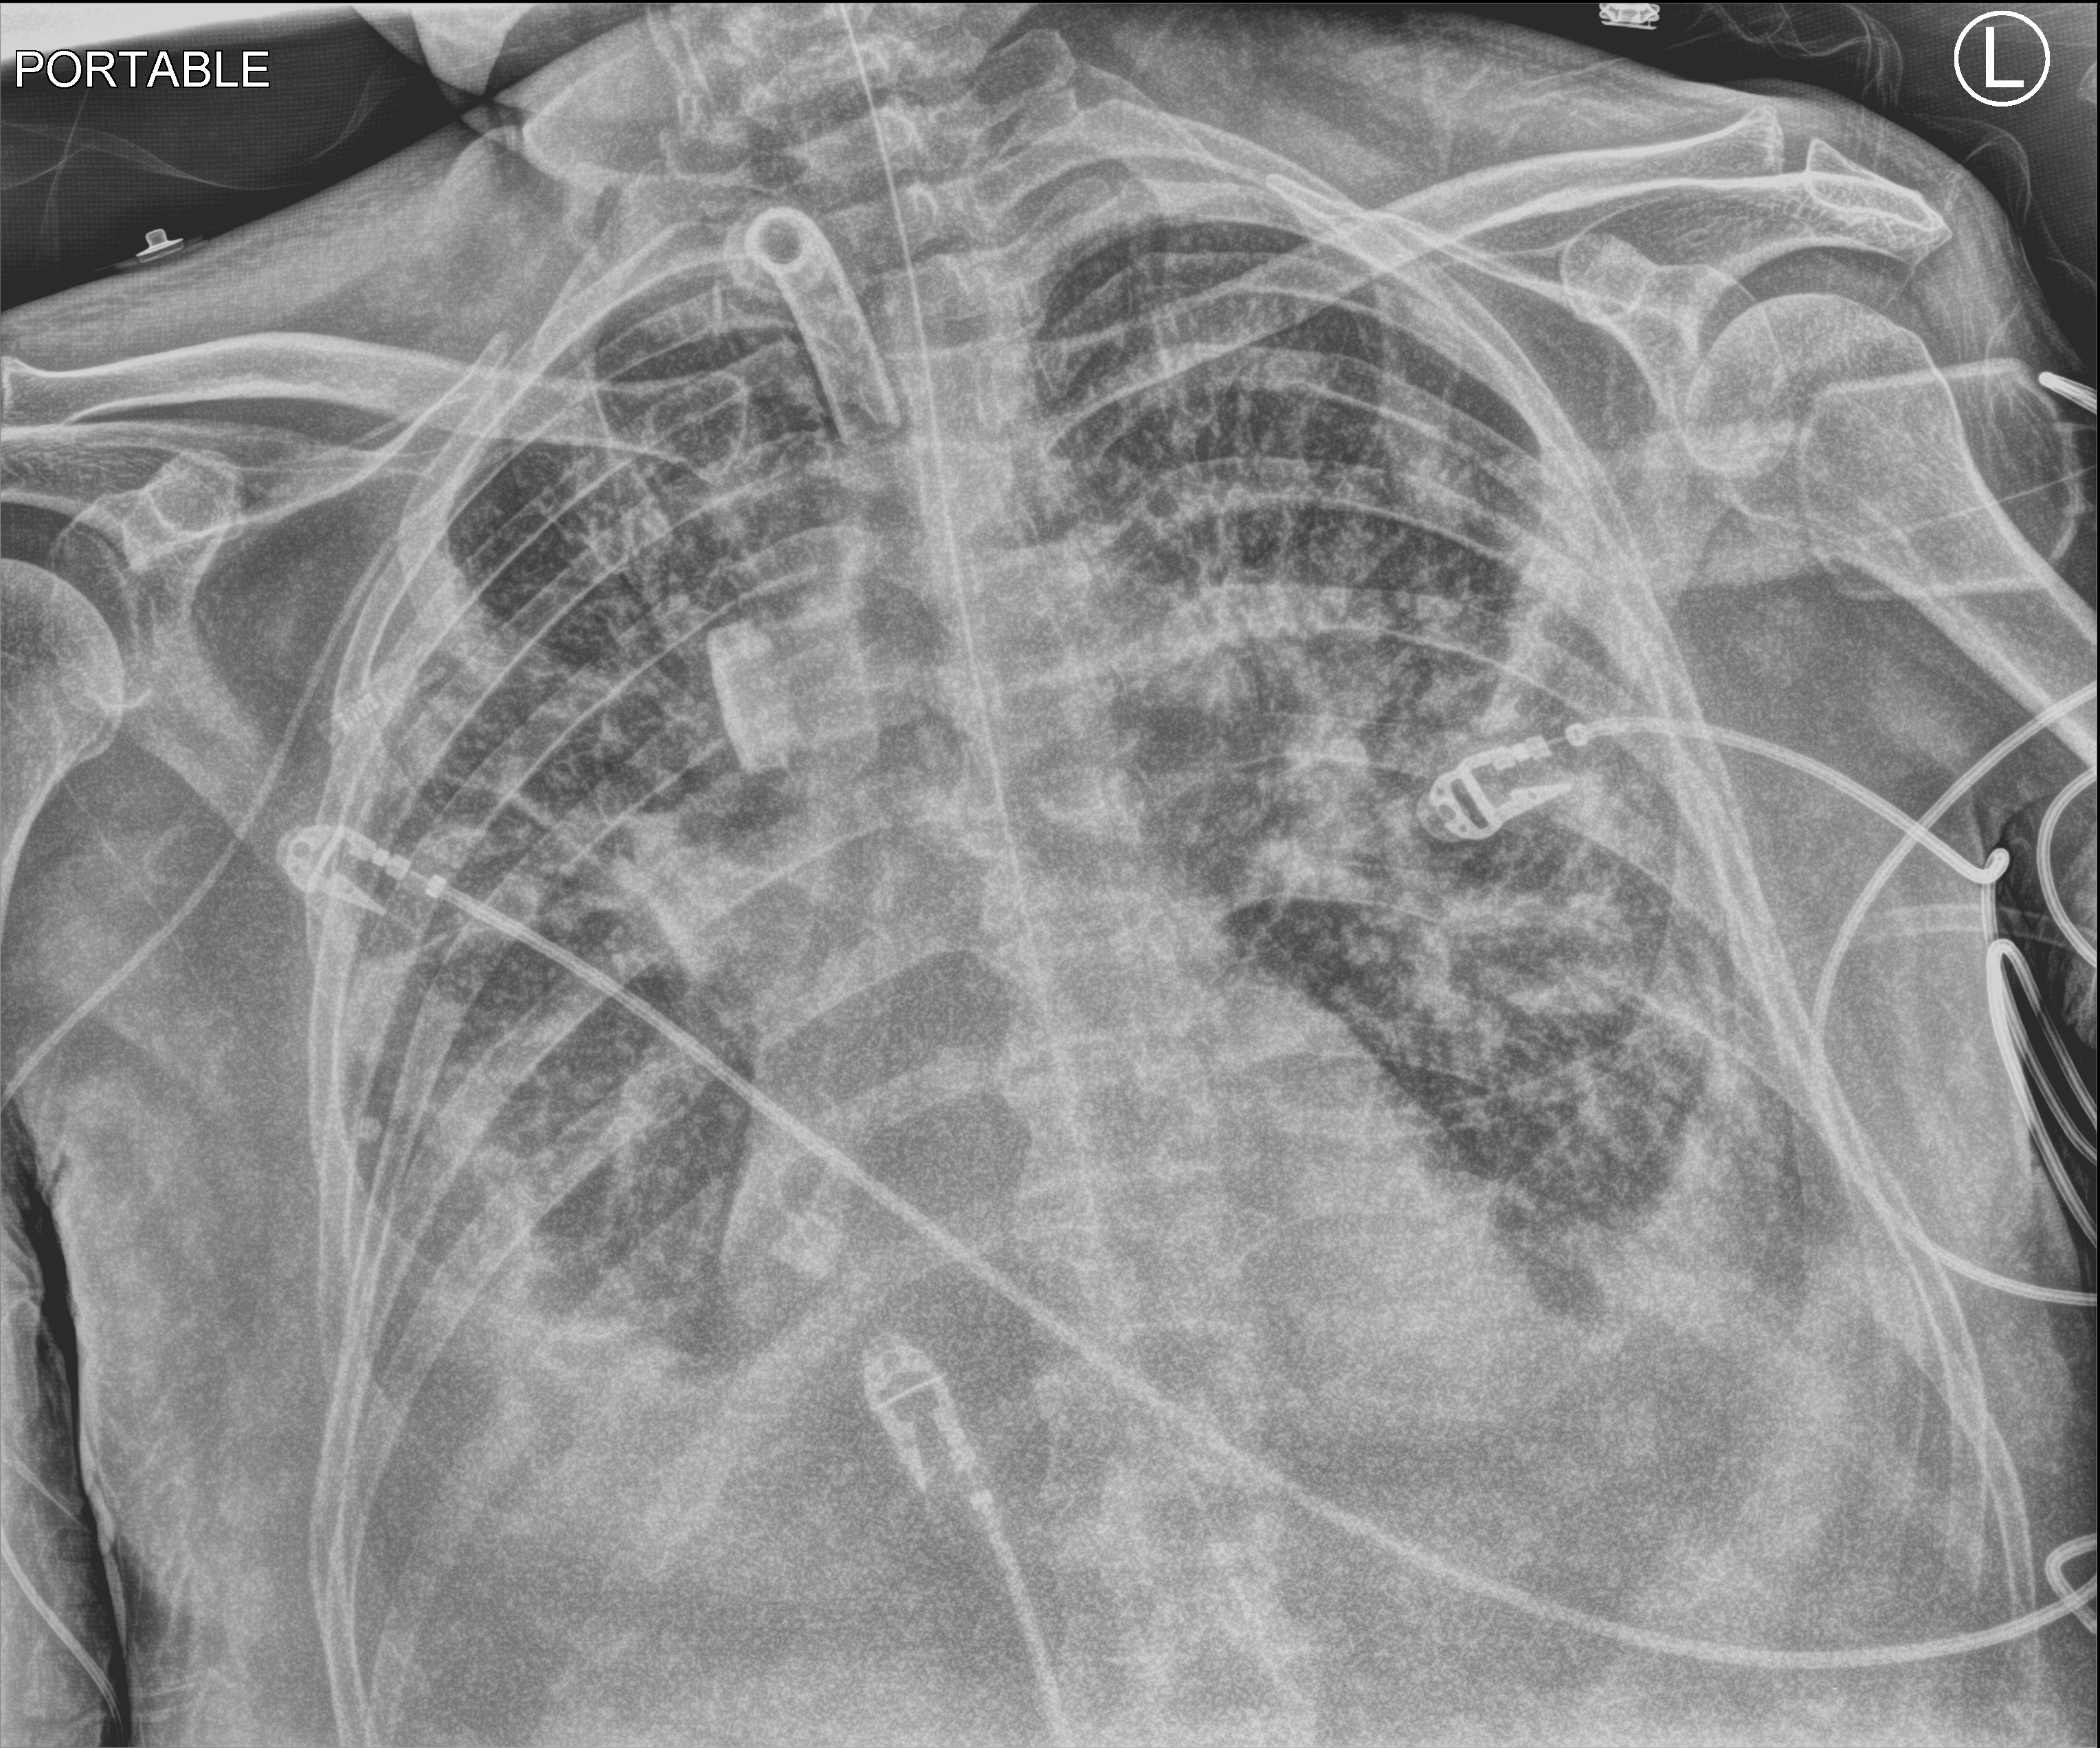
Chest X-ray (portable); anteroposterior (AP) projection. Patient hospitalised with COVID-19; male, aged 75–90 years.
From the hospital-stay record, not from the radiograph (when in the stay this image was taken is not recorded):
- admitted to intensive care during this hospital stay: yes